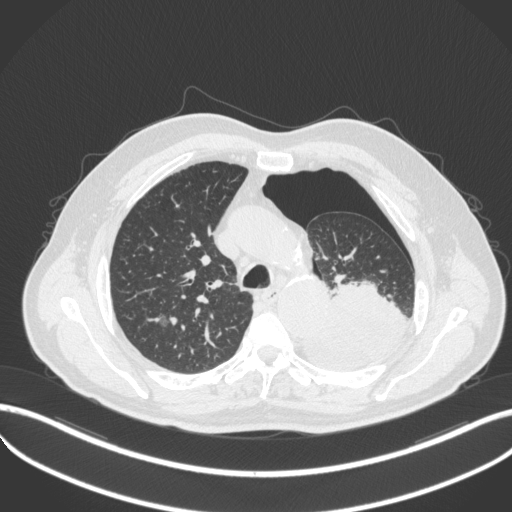
Chest CT, one axial slice; slice 367 of 466 in the series (ordered by position); lung window (W 1500 / L -600 HU); 512 × 512 image matrix. Male patient, age 76 years. From the clinical record (not read from this slice): clinical TNM (as recorded): T3 N0 M1b.
Structures marked on this image (bounding box drawn by a radiologist):
- lung tumour (recorded histology: adenocarcinoma): bounding box [x1, y1, x2, y2] px = [305, 280, 412, 368]